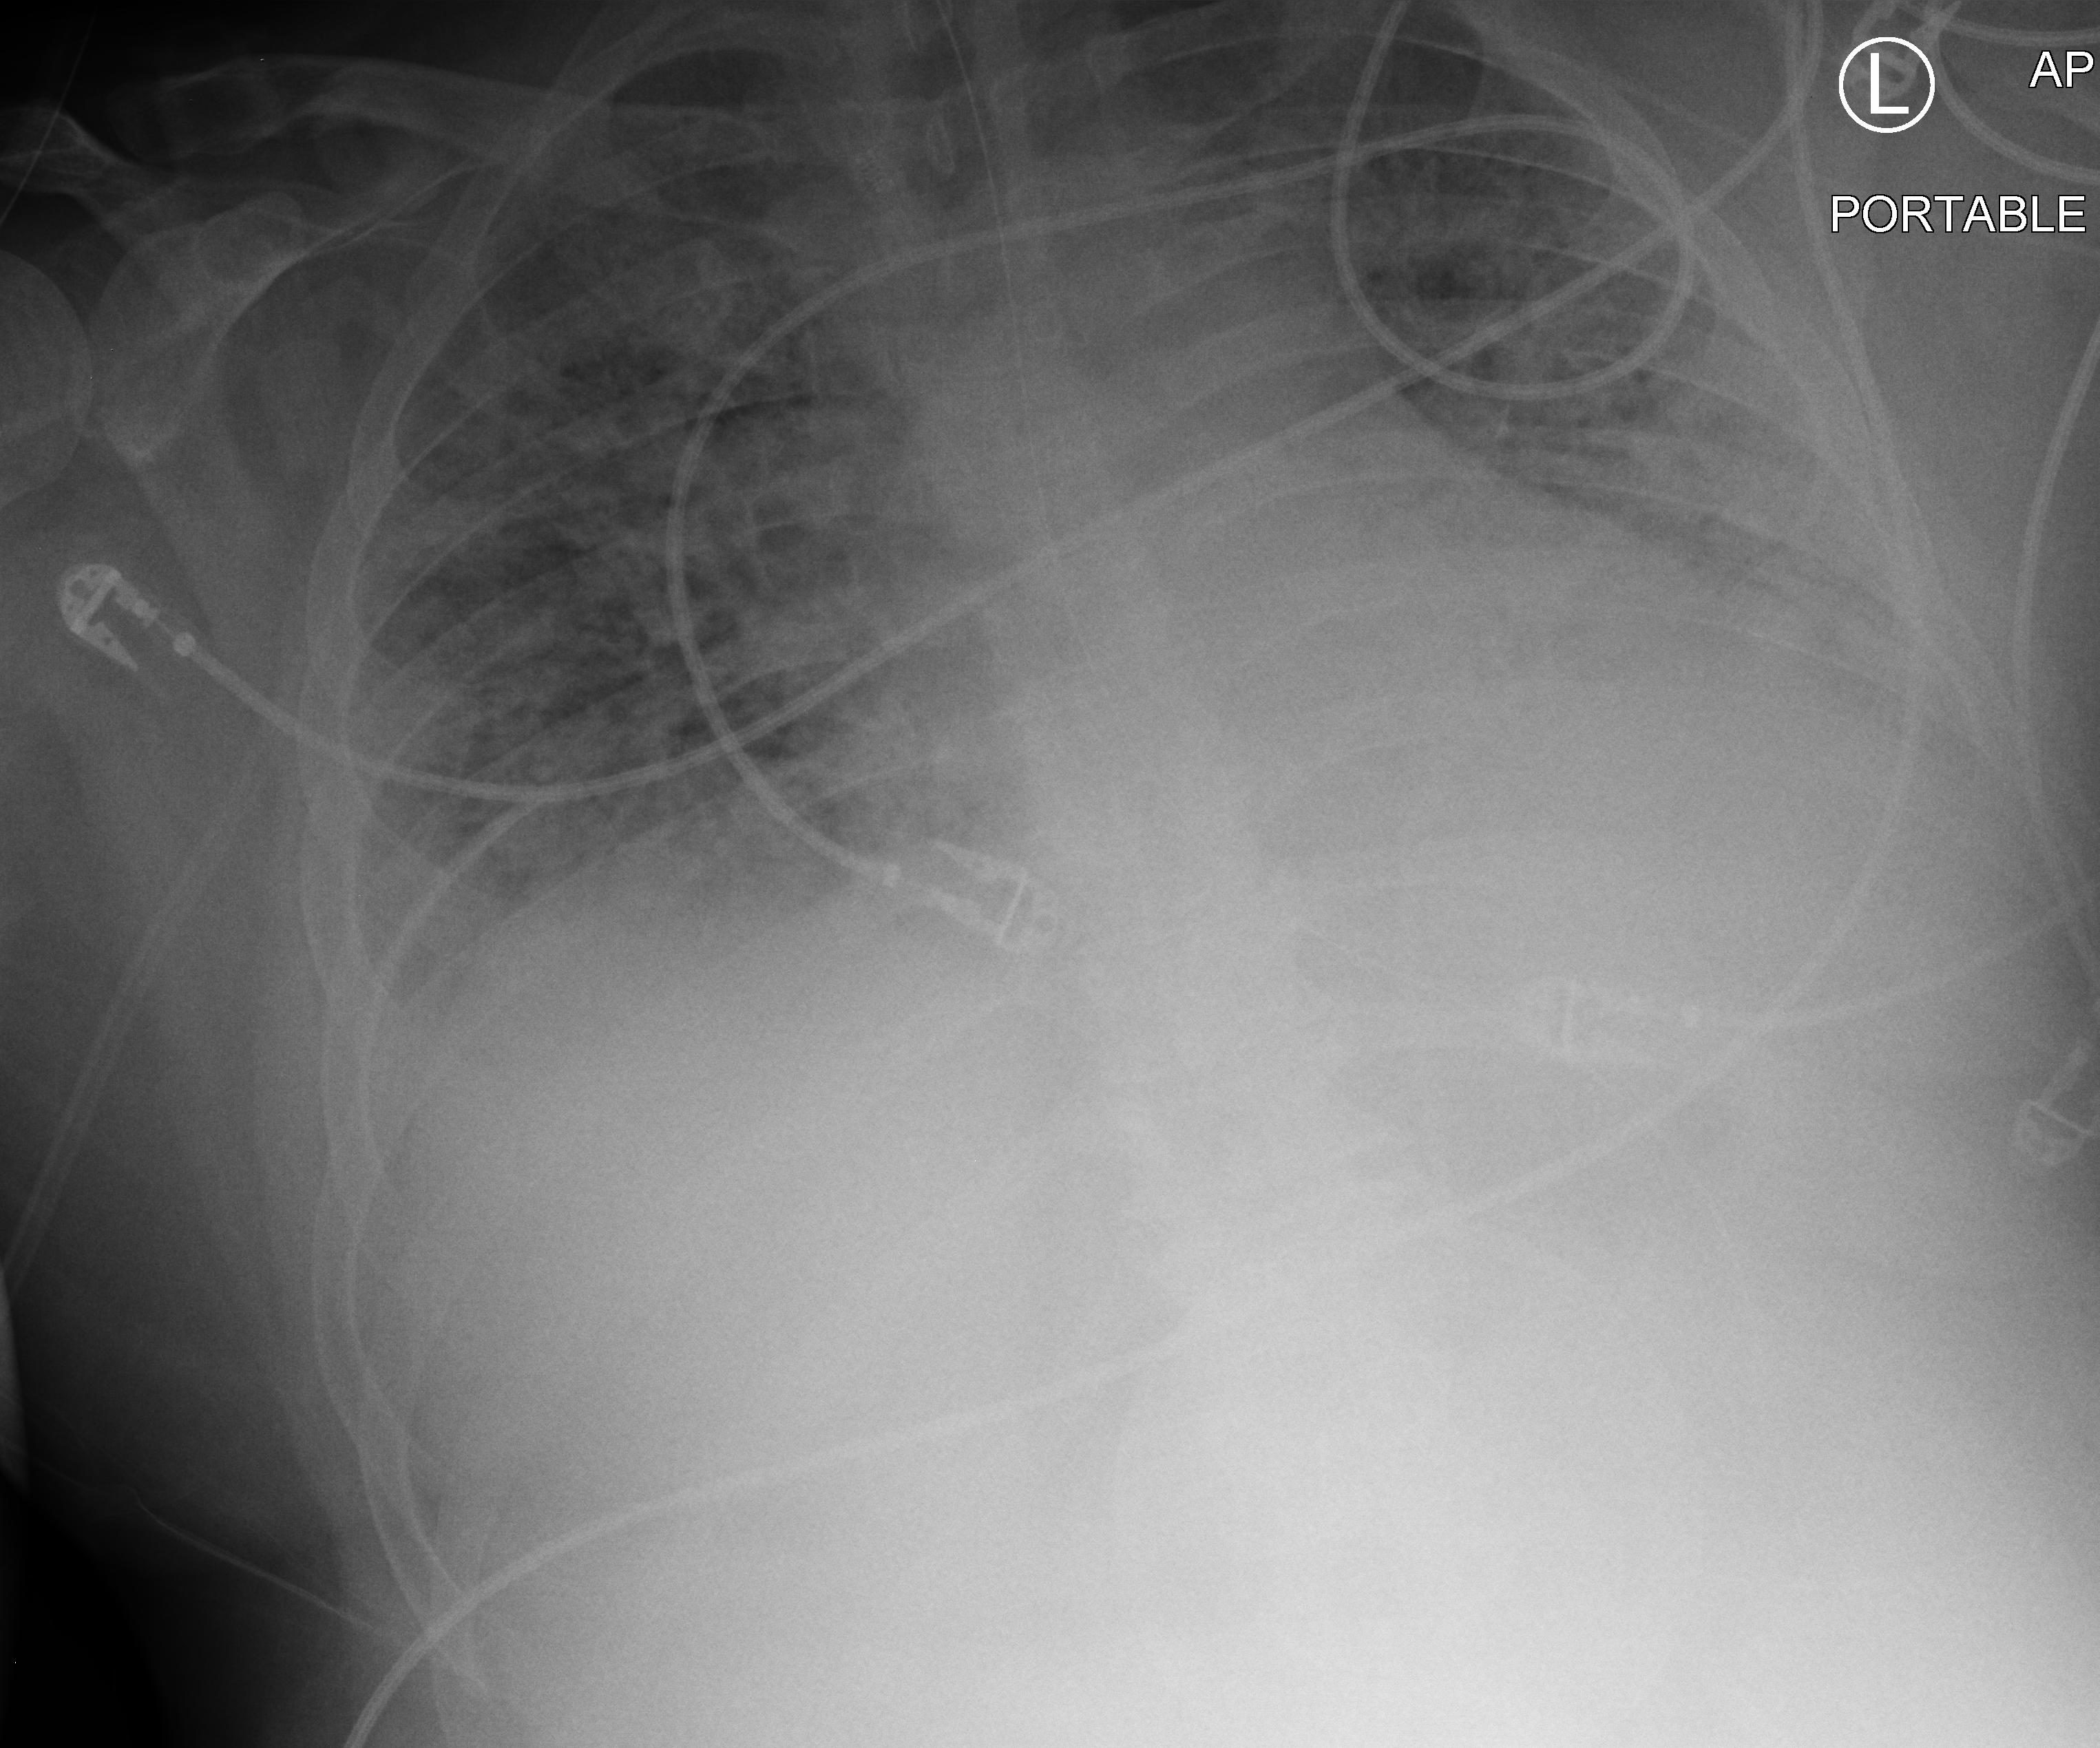
Portable chest radiograph, anteroposterior (AP) projection. Adult patient hospitalised with COVID-19, age 18–59 years.
From the hospital-stay record, not from the radiograph (when in the stay this image was taken is not recorded): admitted to intensive care during this hospital stay: yes.